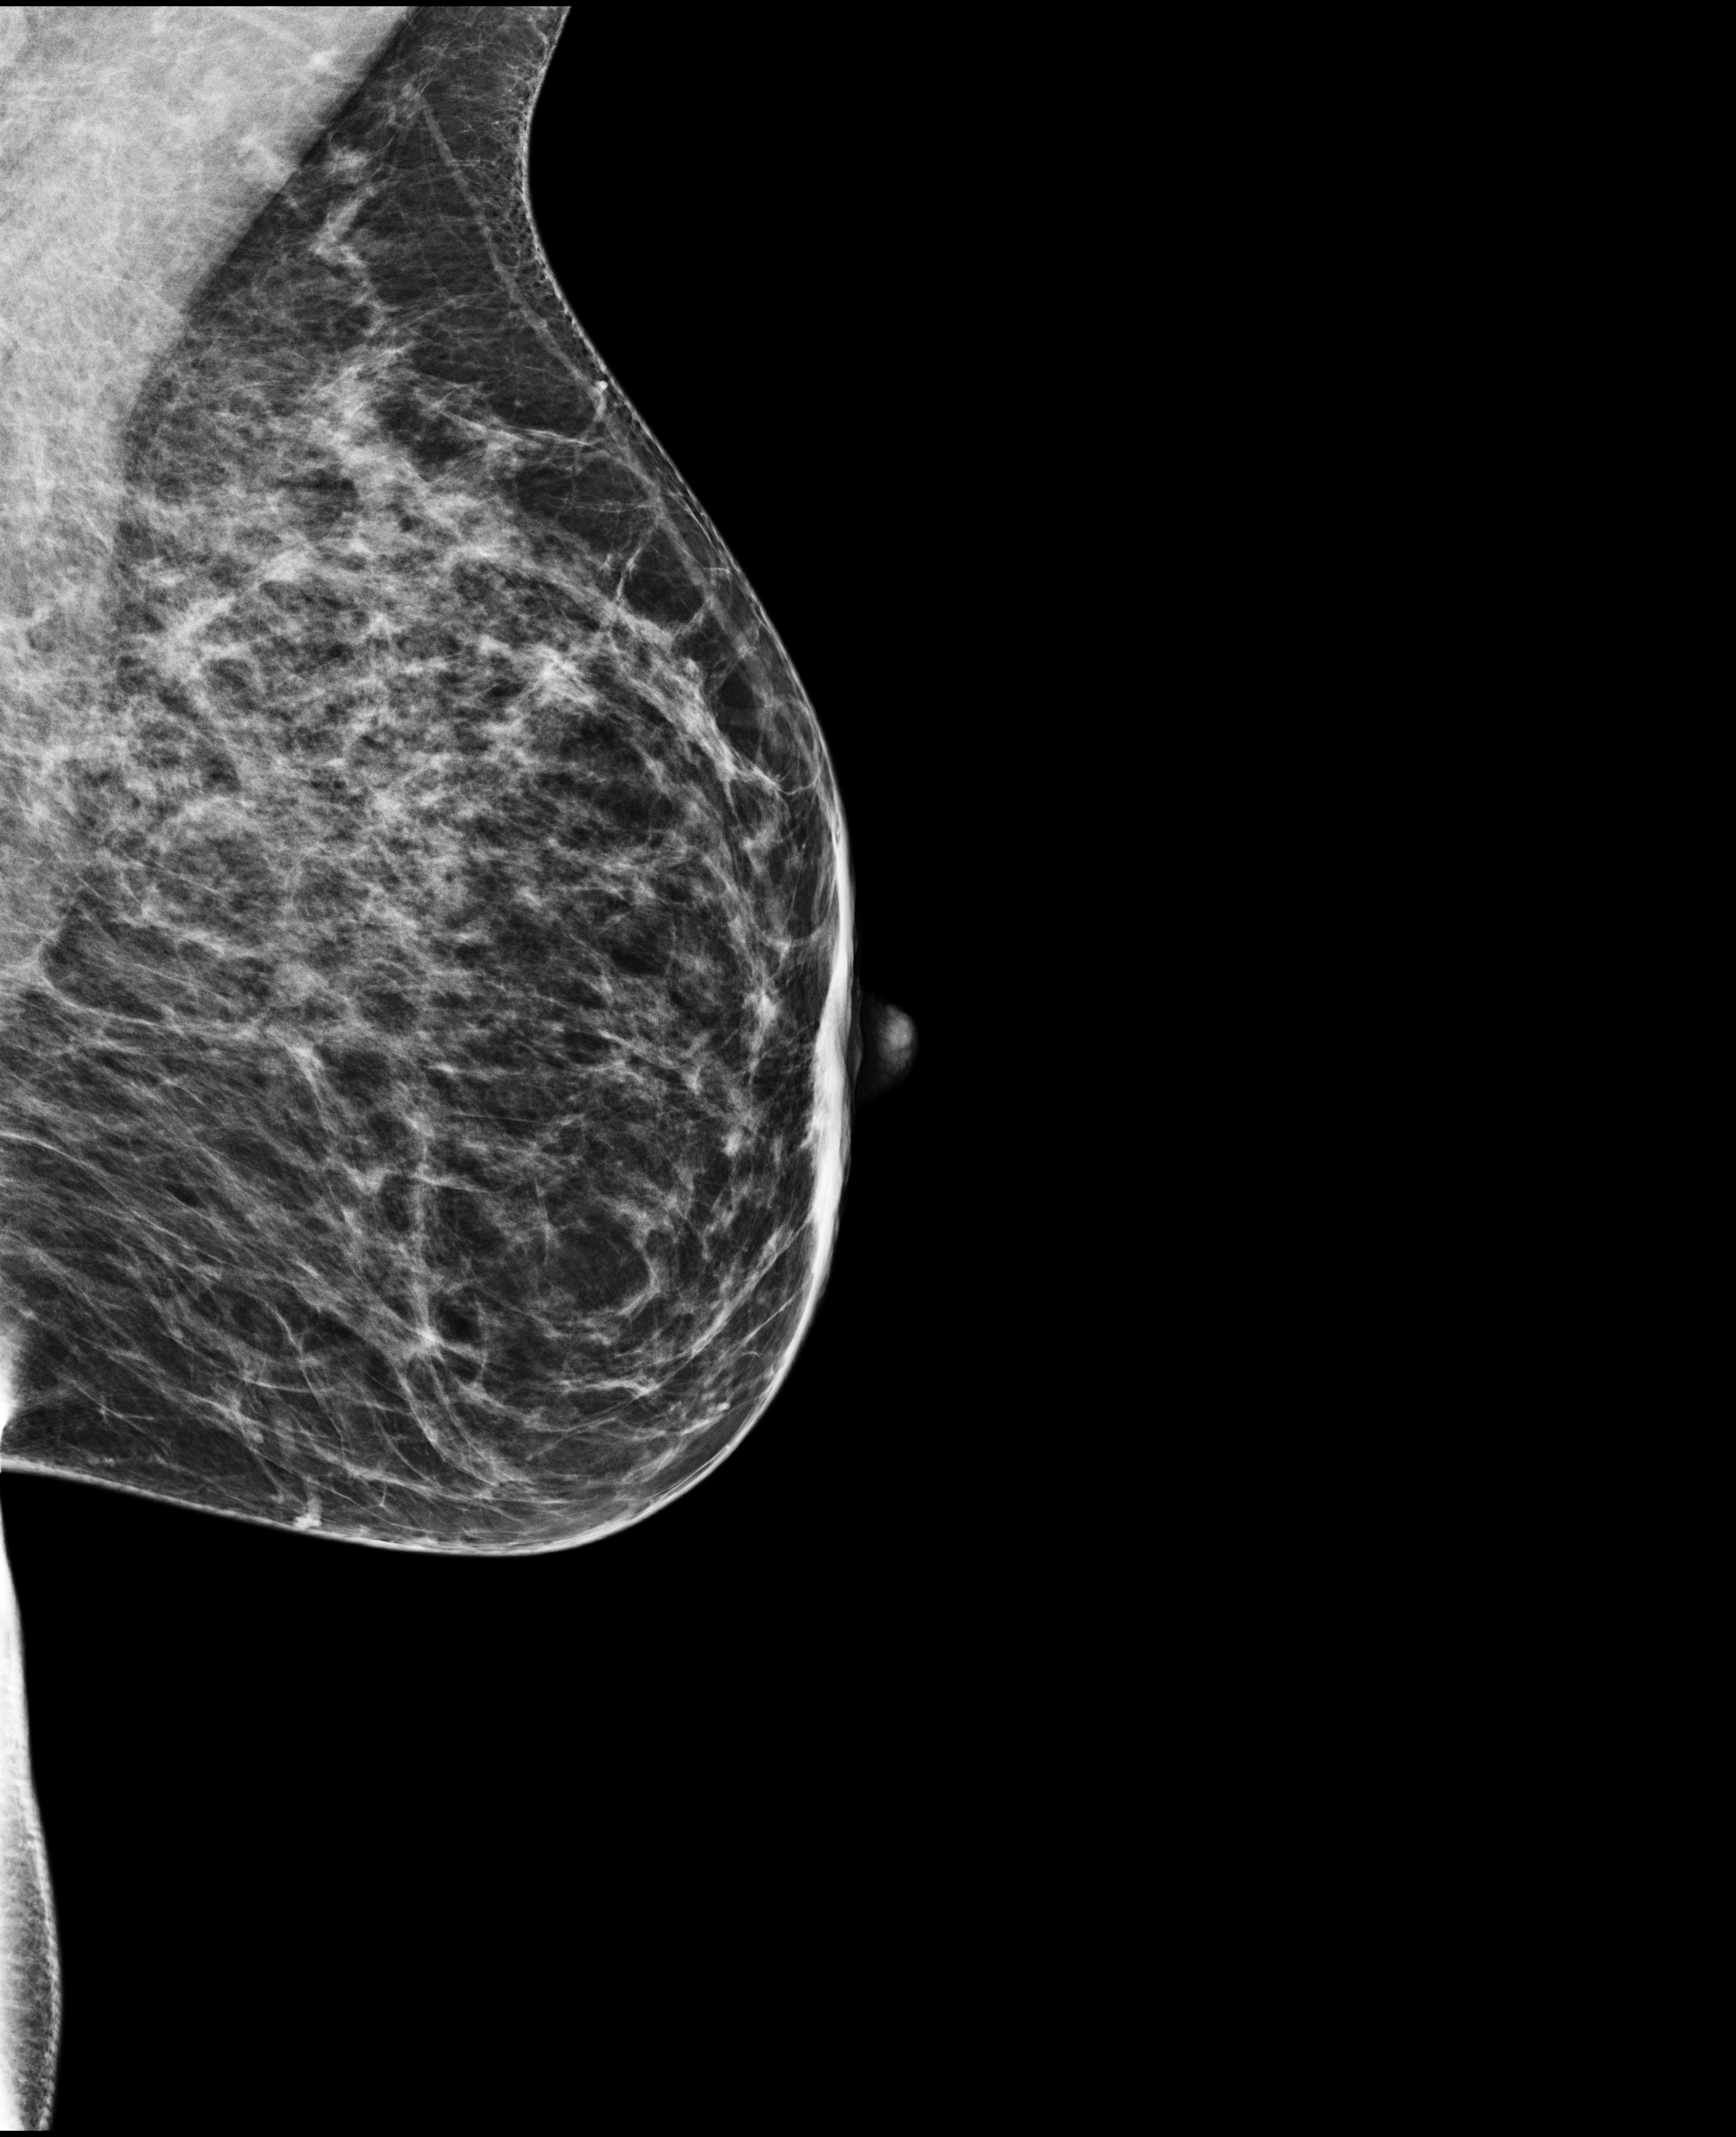
Annual screening mammography examination; compressed breast thickness 56 mm.
Image type: full-field digital mammogram. Breast: left. Projection: mediolateral oblique (MLO) view.